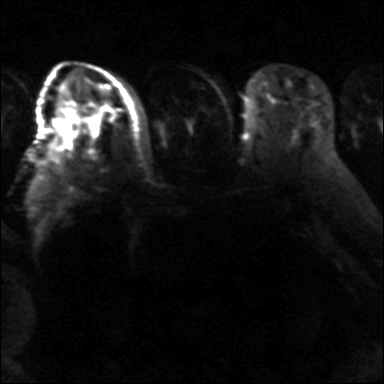
Breast MRI, one axial slice; position 20 of 36 along the scan axis; diffusion-weighted series; image 2 of 4 stored at this slice position (different b-values; order by instance number); 3 T; 4 mm slice thickness; 384 × 384 image matrix, field of view 320 × 320 mm. Female patient.
Annotated regions visible in this slice (manually delineated by an expert):
- tumour on diffusion-weighted imaging: bounding box (x1, y1, x2, y2) in pixels: (66, 136, 73, 145)